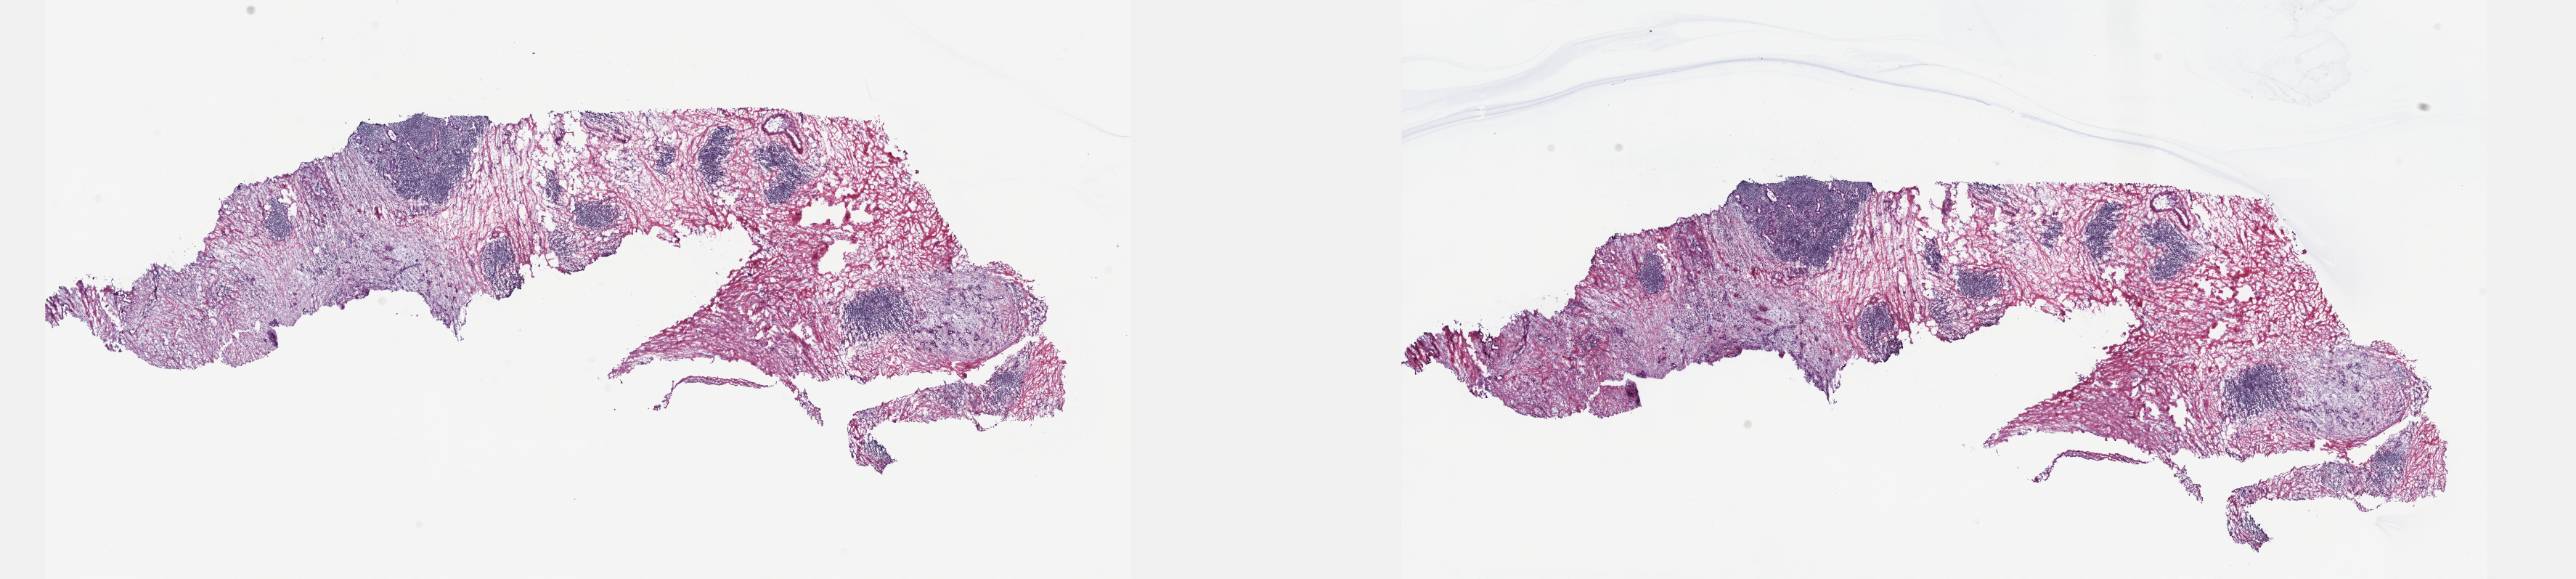
Whole-slide histology image, Hematoxylin and eosin (H&E) stained — whole scanned area (about 28.7 x 6.4 mm, from a 40x scan) shown as a low-resolution overview, frozen section from the top of the tissue portion, pancreas, primary tumour sample. Male, age 68 years at initial diagnosis. Histologic grade: G2 (moderately differentiated). Composition of this section per pathologist review: tumour cells 15%, tumour nuclei 15%, normal cells 5%, stromal cells 80%, necrosis 0%. Inflammatory infiltration, as recorded: lymphocyte infiltration 10%, monocyte infiltration 2%, neutrophil infiltration 8%.
- AJCC pathologic stage: IIB
- diagnosis: Infiltrating duct carcinoma, NOS (head of pancreas)